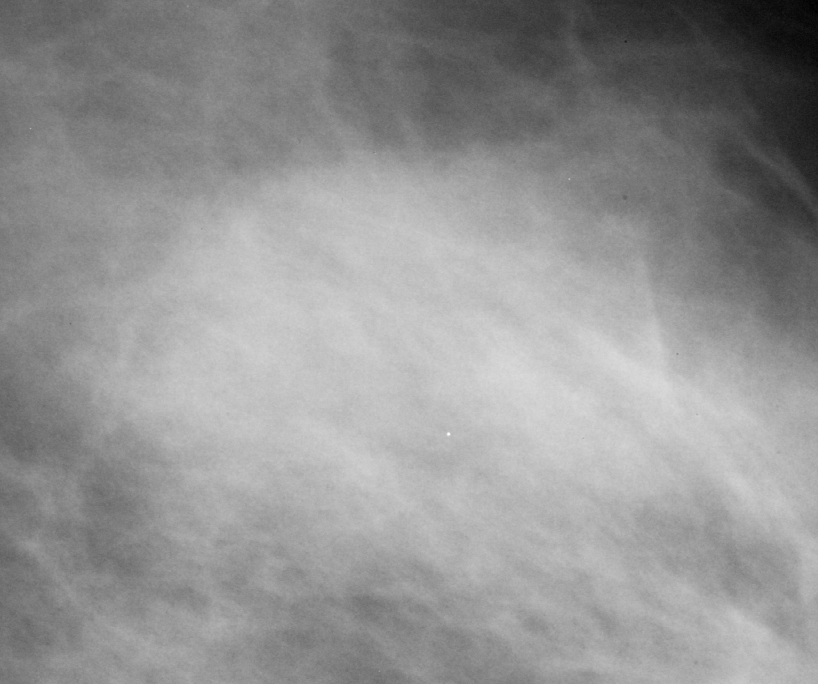
Cropped region of a digitized screen-film mammogram centred on a radiologist-marked abnormality, left breast, MLO view.
Mass, shape asymmetric breast tissue; BI-RADS assessment category 3; benign; no additional work-up was recommended (benign without callback).